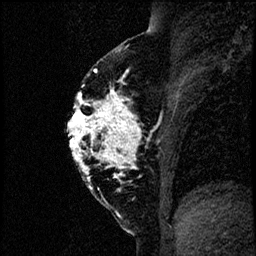
Breast MRI (dynamic contrast-enhanced), one sagittal slice; position 38 of 60 along the scan axis; dynamic contrast-enhanced study with each time point stored as its own series, time point 2 of 4 at this slice position (early post-contrast, ordered by acquisition time); 1.5 T; TE 4.2 ms, TR 17.6 ms; 2 mm slice thickness; 256 × 256 image matrix. Patient: female, 40 years. Case-level facts recorded for this patient, not image findings: setting: breast cancer imaged before/during neoadjuvant chemotherapy; receptor status: HER2-positive.
Outlined on this slice (semi-automatically segmented with operator editing):
- analysis volume of interest (the breast-tissue region the enhancement analysis was run in; not a lesion): bounding box (x1, y1, x2, y2) in pixels: (66, 55, 185, 206)
- tumour enhancement mask (voxels above the 100 % enhancement threshold inside the analysis volume of interest): (68, 69, 138, 180)